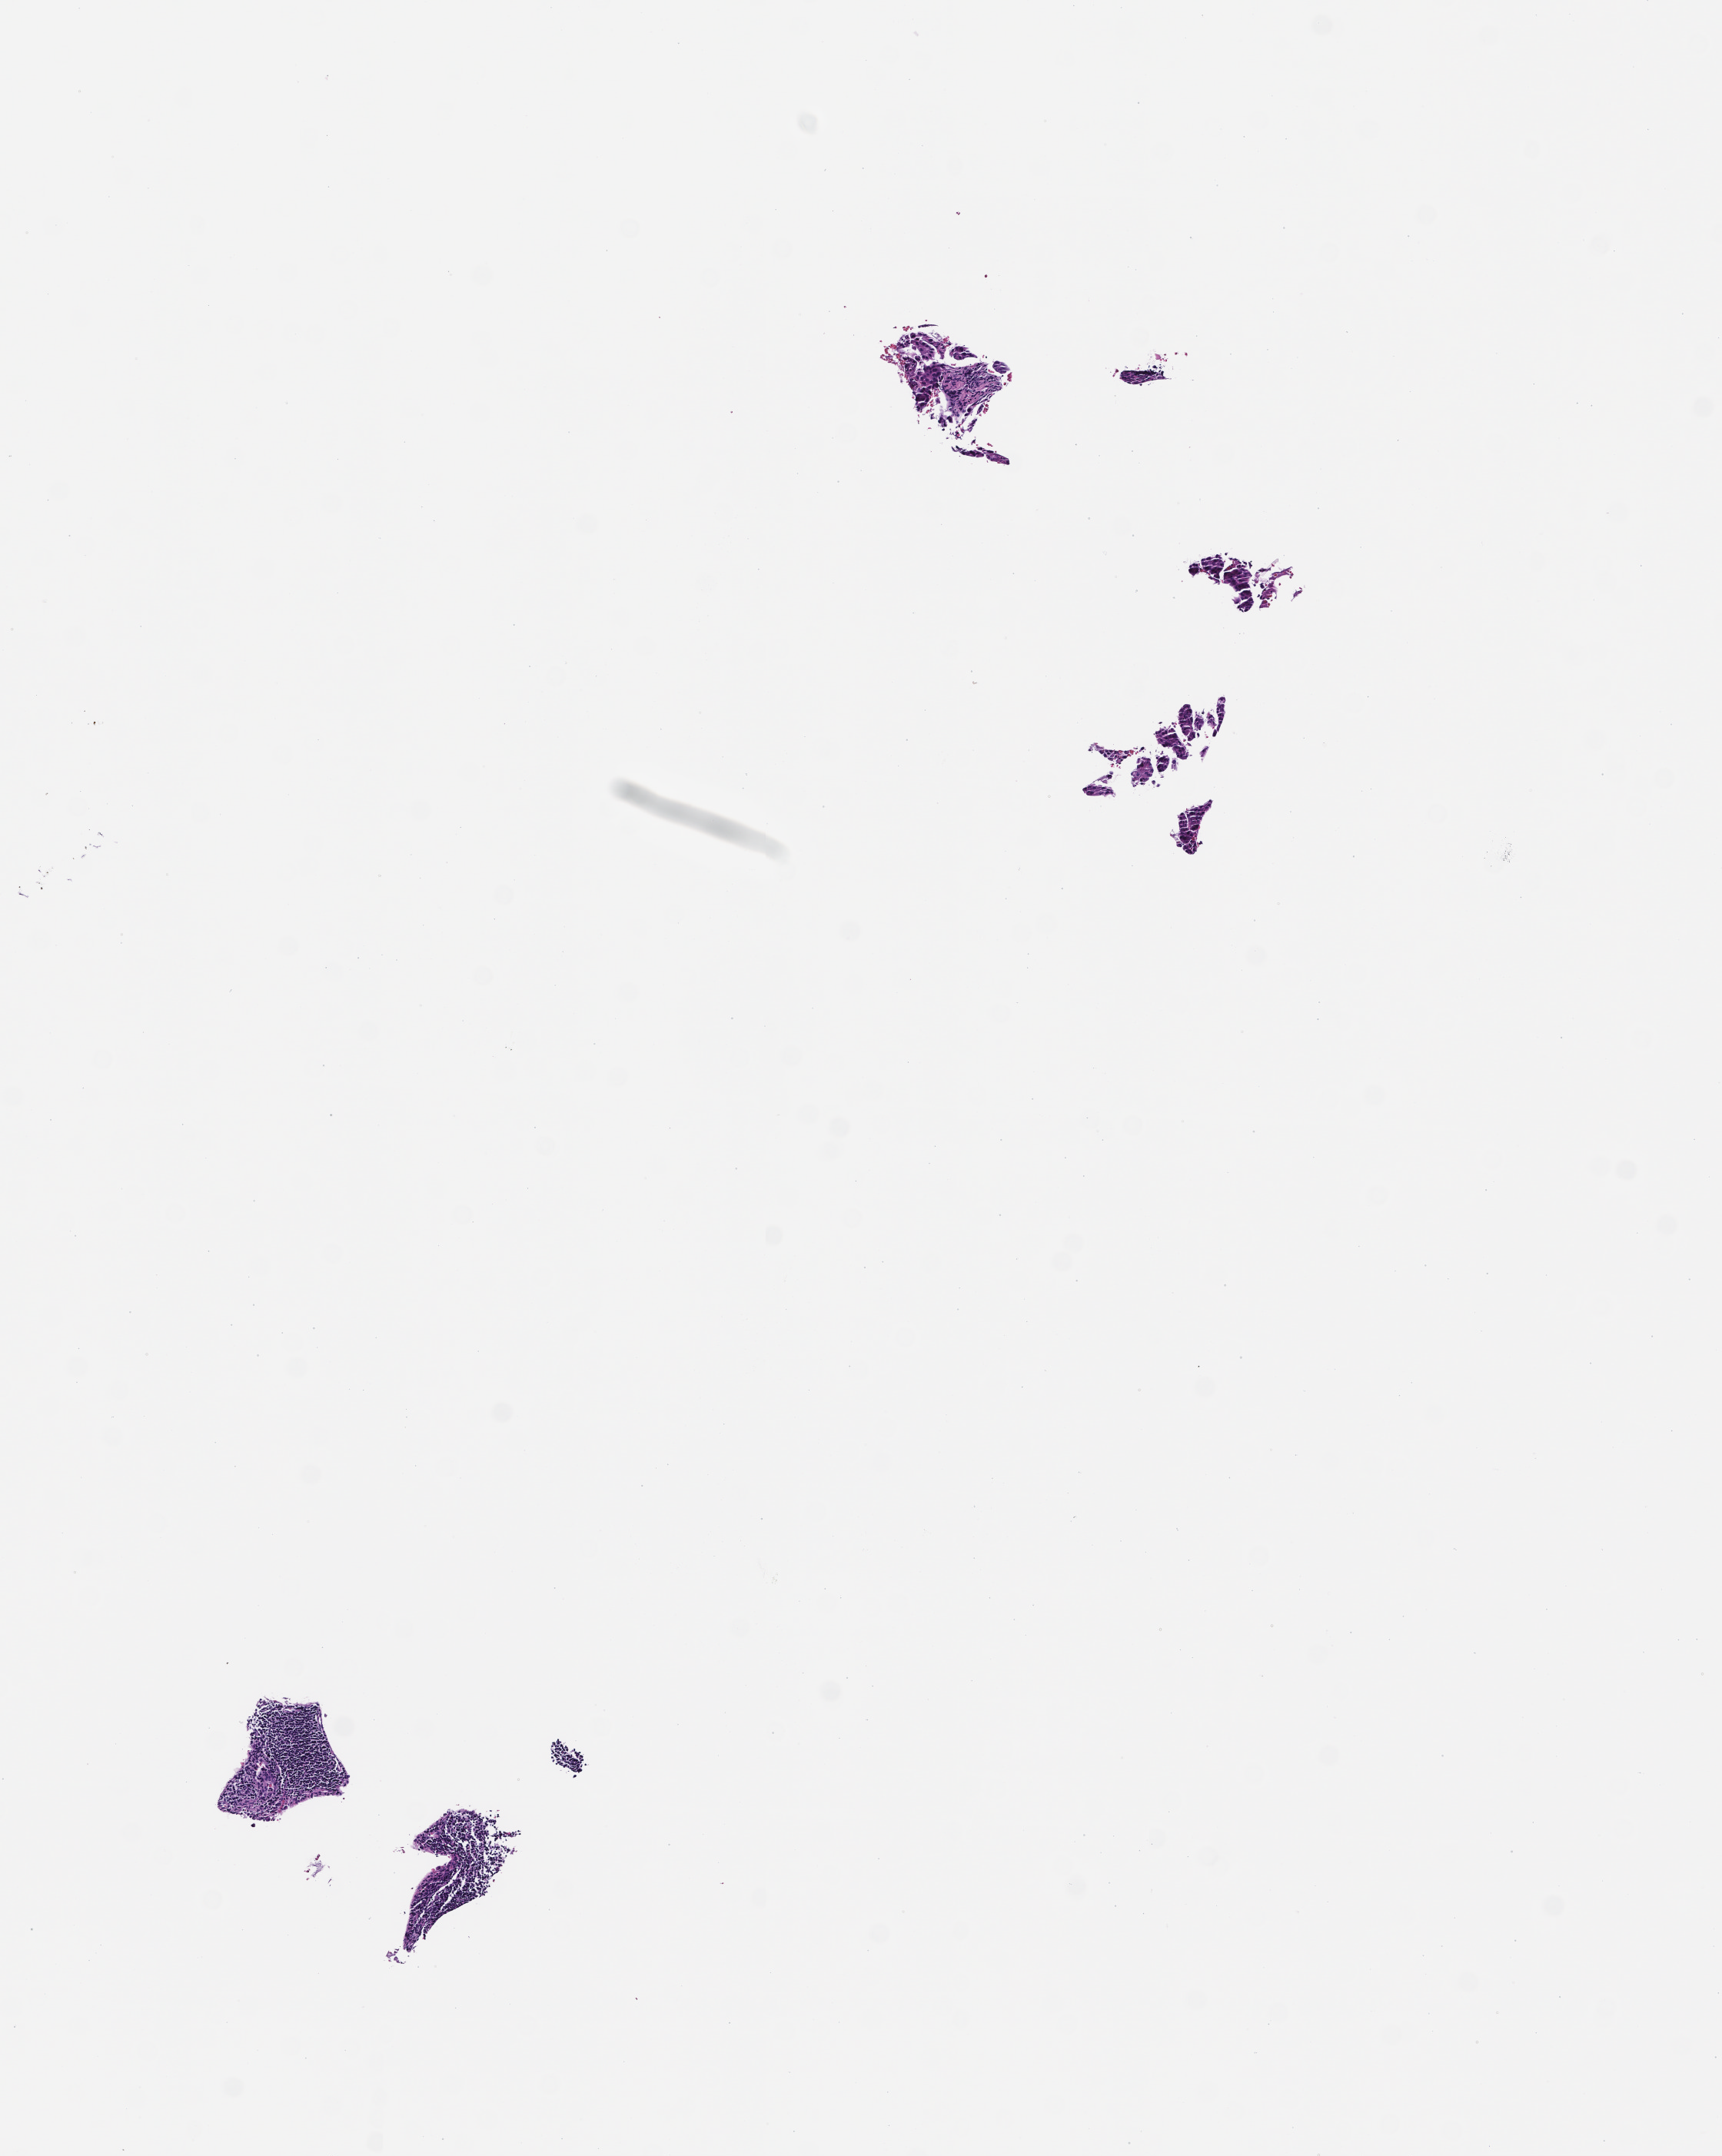
Whole-slide image, haematoxylin and eosin stain — whole scanned area (about 4.5 x 5.7 mm) shown as a low-resolution overview, FFPE section, collected at baseline (before treatment). Patient sex: female.
This section: metastatic tumor tissue. Primary diagnosis of the patient: Small Cell Lung Carcinoma.